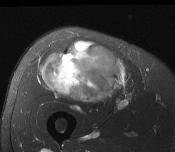
MRI of an extremity soft-tissue mass, one axial slice; slice 81 of 116 in the series (ordered by position); T2-weighted fat-saturated; MR volume resampled by the dataset authors to the PET/CT grid (not the native acquisition matrix); 175 × 152 image matrix, field of view 171 × 148 mm. Male patient. From the clinical record (not read from this slice): histological type: pleiomorphic leiomyosarcoma; grade: intermediate; site of the primary tumour: right thigh.
Outlined on this slice (expert contour drawn on MRI and transferred to this co-registered scan by the dataset authors):
- gross tumour volume including surrounding oedema: box from (x=42, y=42) to (x=126, y=103) px
- gross tumour volume (mass): (x=42, y=42)–(x=126, y=103)